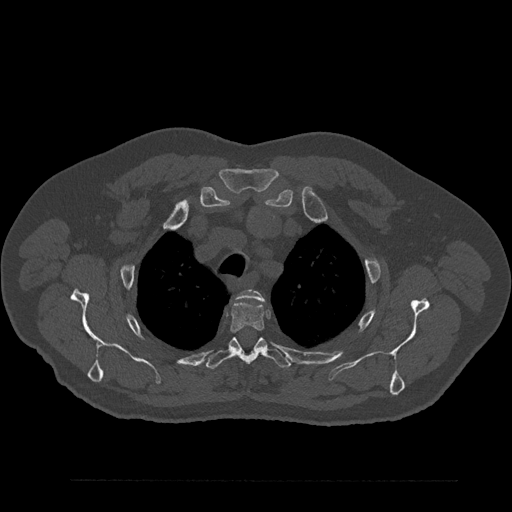
CT including the spine, one axial slice. Slice 669 of 797 in the series (ordered by position). Reconstruction kernel Br40s/3. 120 kVp. Bone window (W 1800 / L 400 HU). 0.5 mm slice thickness. 512 × 512 image matrix. Male patient, age 61 years. From the clinical record (not read from this slice): primary cancer: prostate.
Annotated regions visible in this slice (semi-automatically segmented with operator editing):
- T2 vertebra: bounding box <238,290,264,301> (left, top, right, bottom; pixels)
- T3 vertebra: <230,301,264,333>
- T4 vertebra: <207,337,291,370>